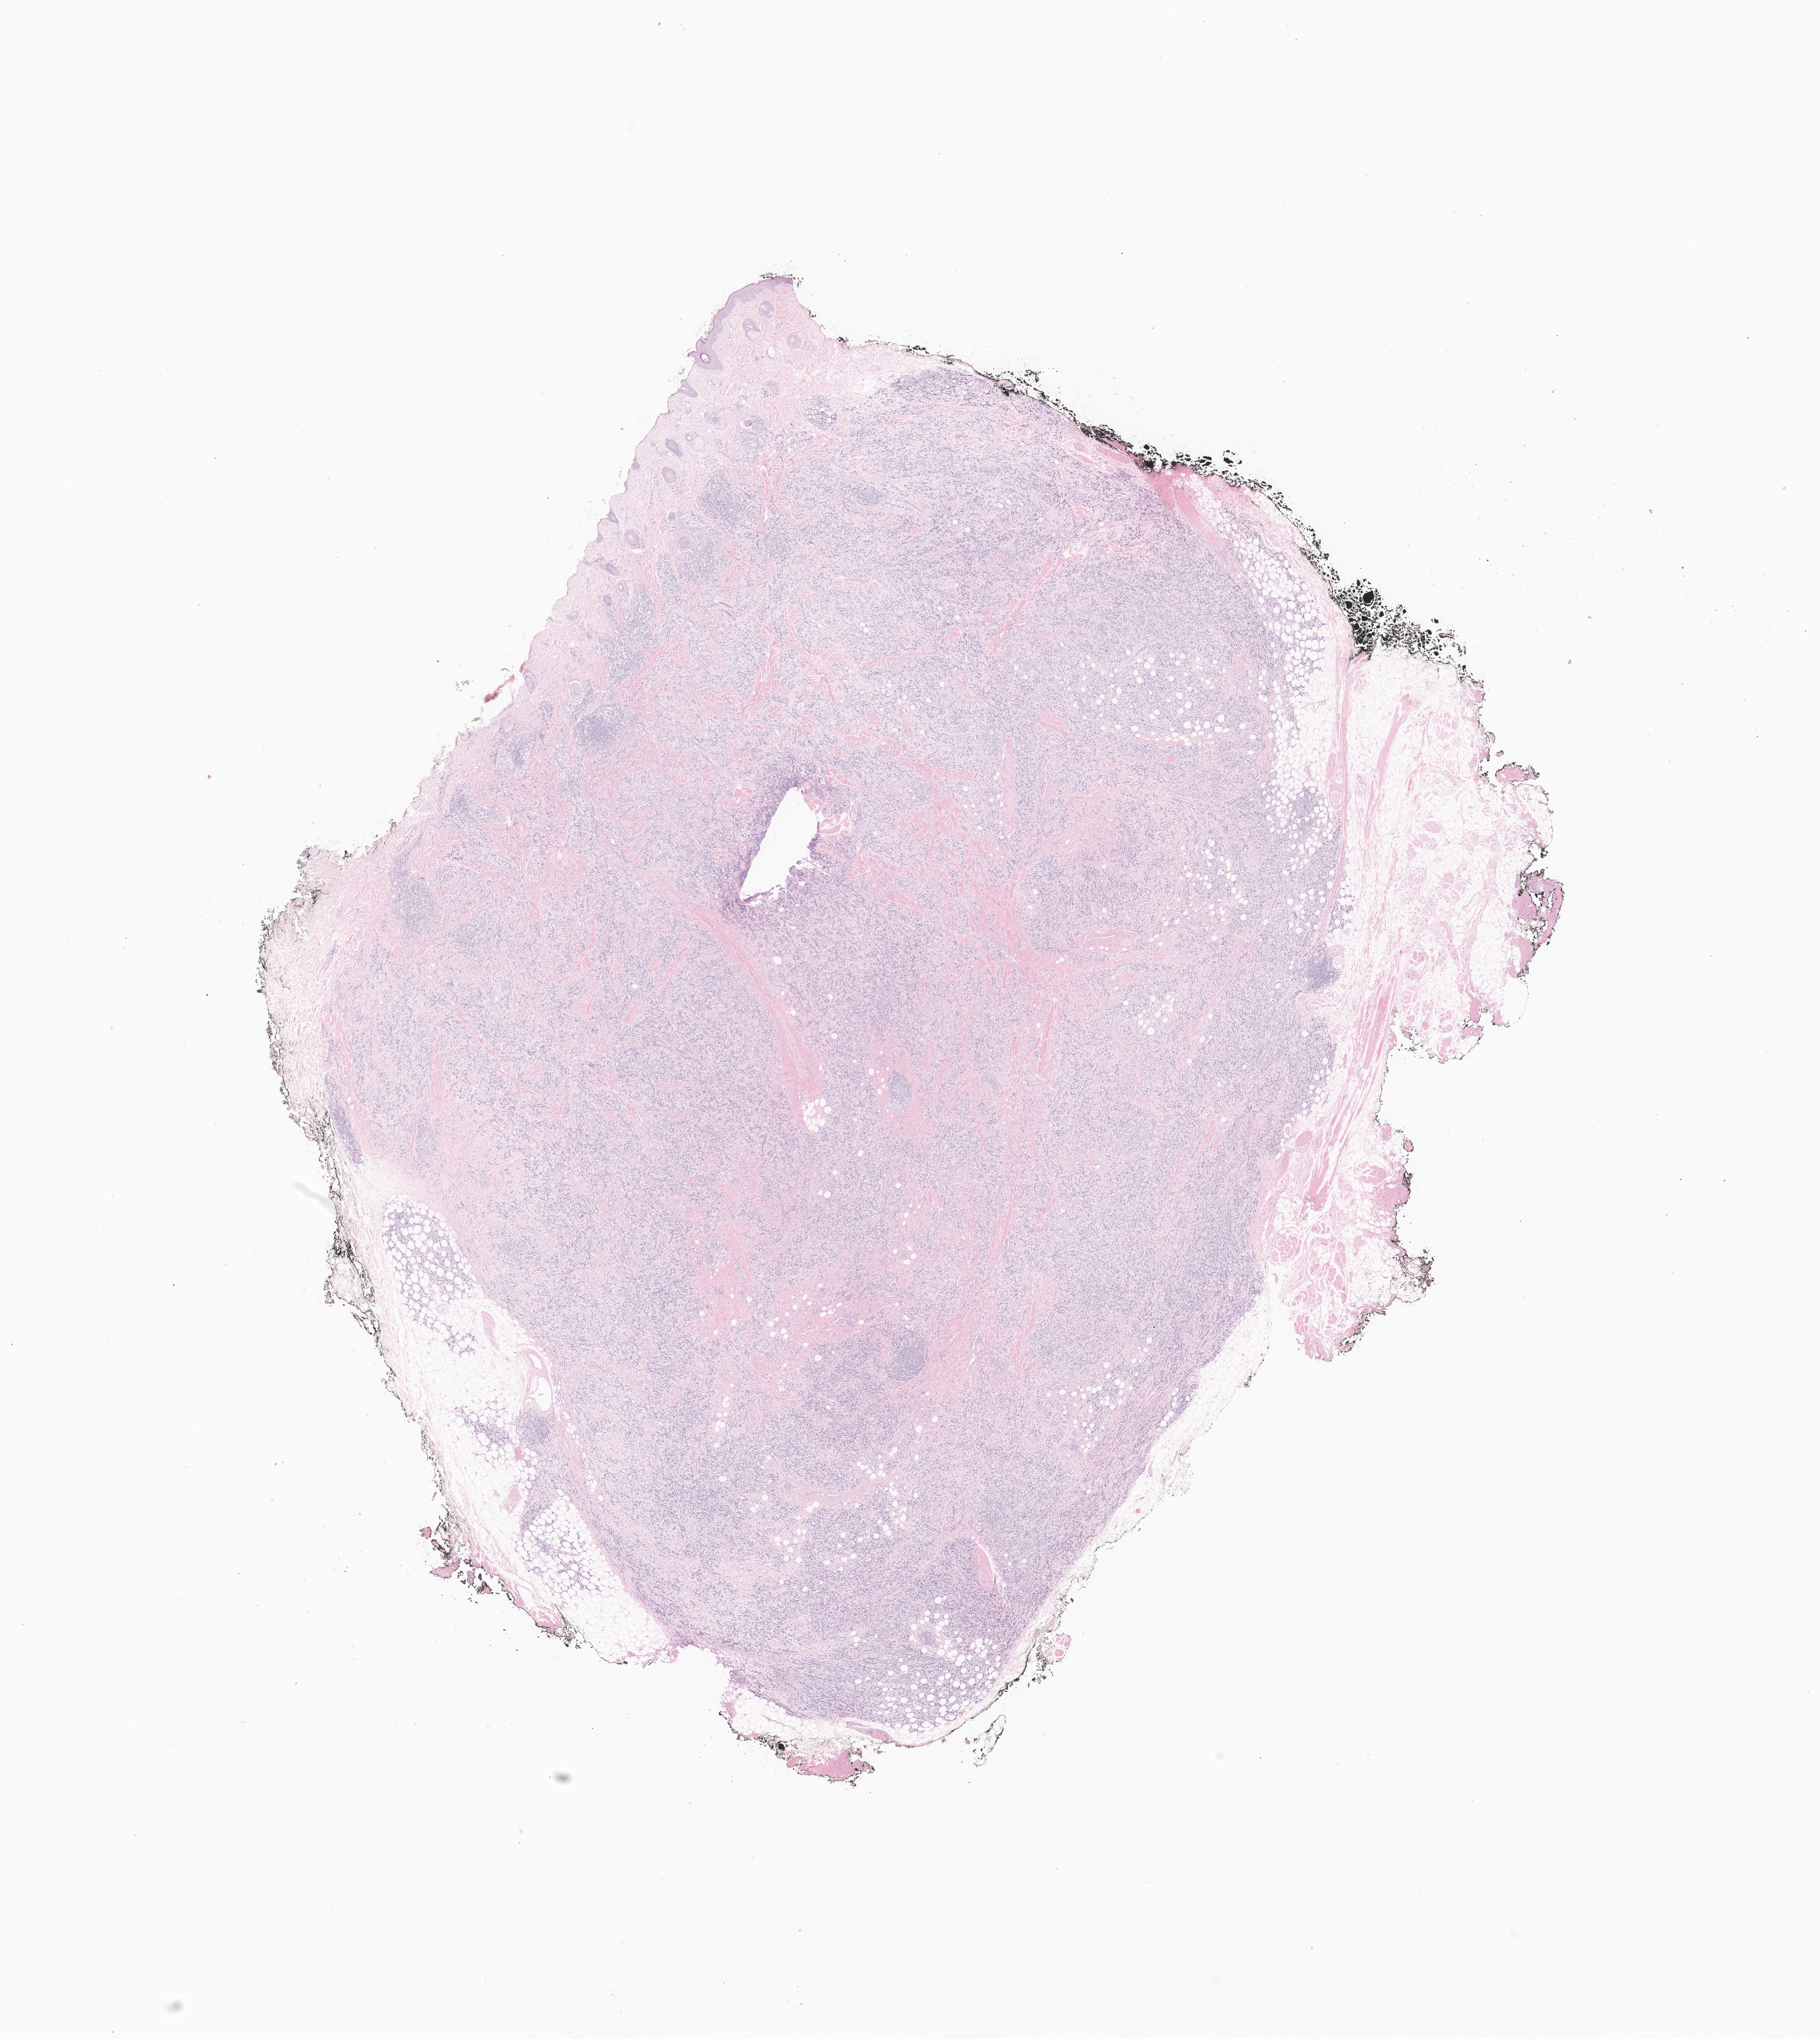
Whole-slide image, H&E stain of tumor tissue from the head and neck — whole scanned area (about 13.8 x 15.5 mm) shown as a low-resolution overview; formalin-fixed, paraffin-embedded (FFPE) tissue. Patient female; age 140 months (11 years 8 months).
Tissue or organ of origin (case record): head, face or neck. Diagnosis (ICD-O-3 morphology term): Rhabdomyosarcoma, NOS.